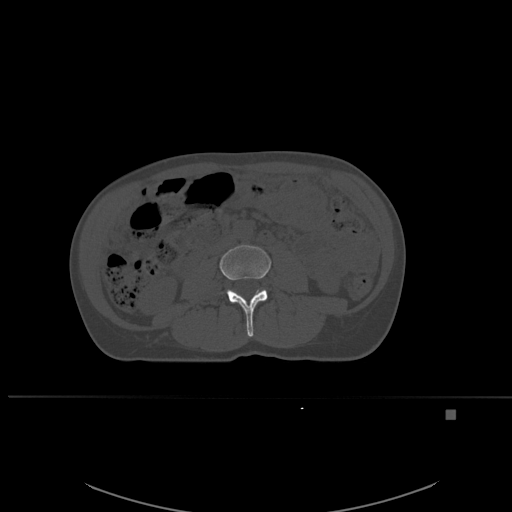
CT including the spine, one axial slice. Slice 210 of 537 in the series (ordered by position). Bone window (W 1800 / L 400 HU). 1.5 mm slice thickness. 512 × 512 image matrix, field of view 440 × 440 mm. Patient: female, 45 years. From the clinical record (not read from this slice): primary cancer: lung.
Outlined on this slice (semi-automatic segmentation, software-assisted and operator-edited):
- L3 vertebra: box from (x=220, y=245) to (x=271, y=337) px
- L4 vertebra: (x=231, y=290)–(x=233, y=292)